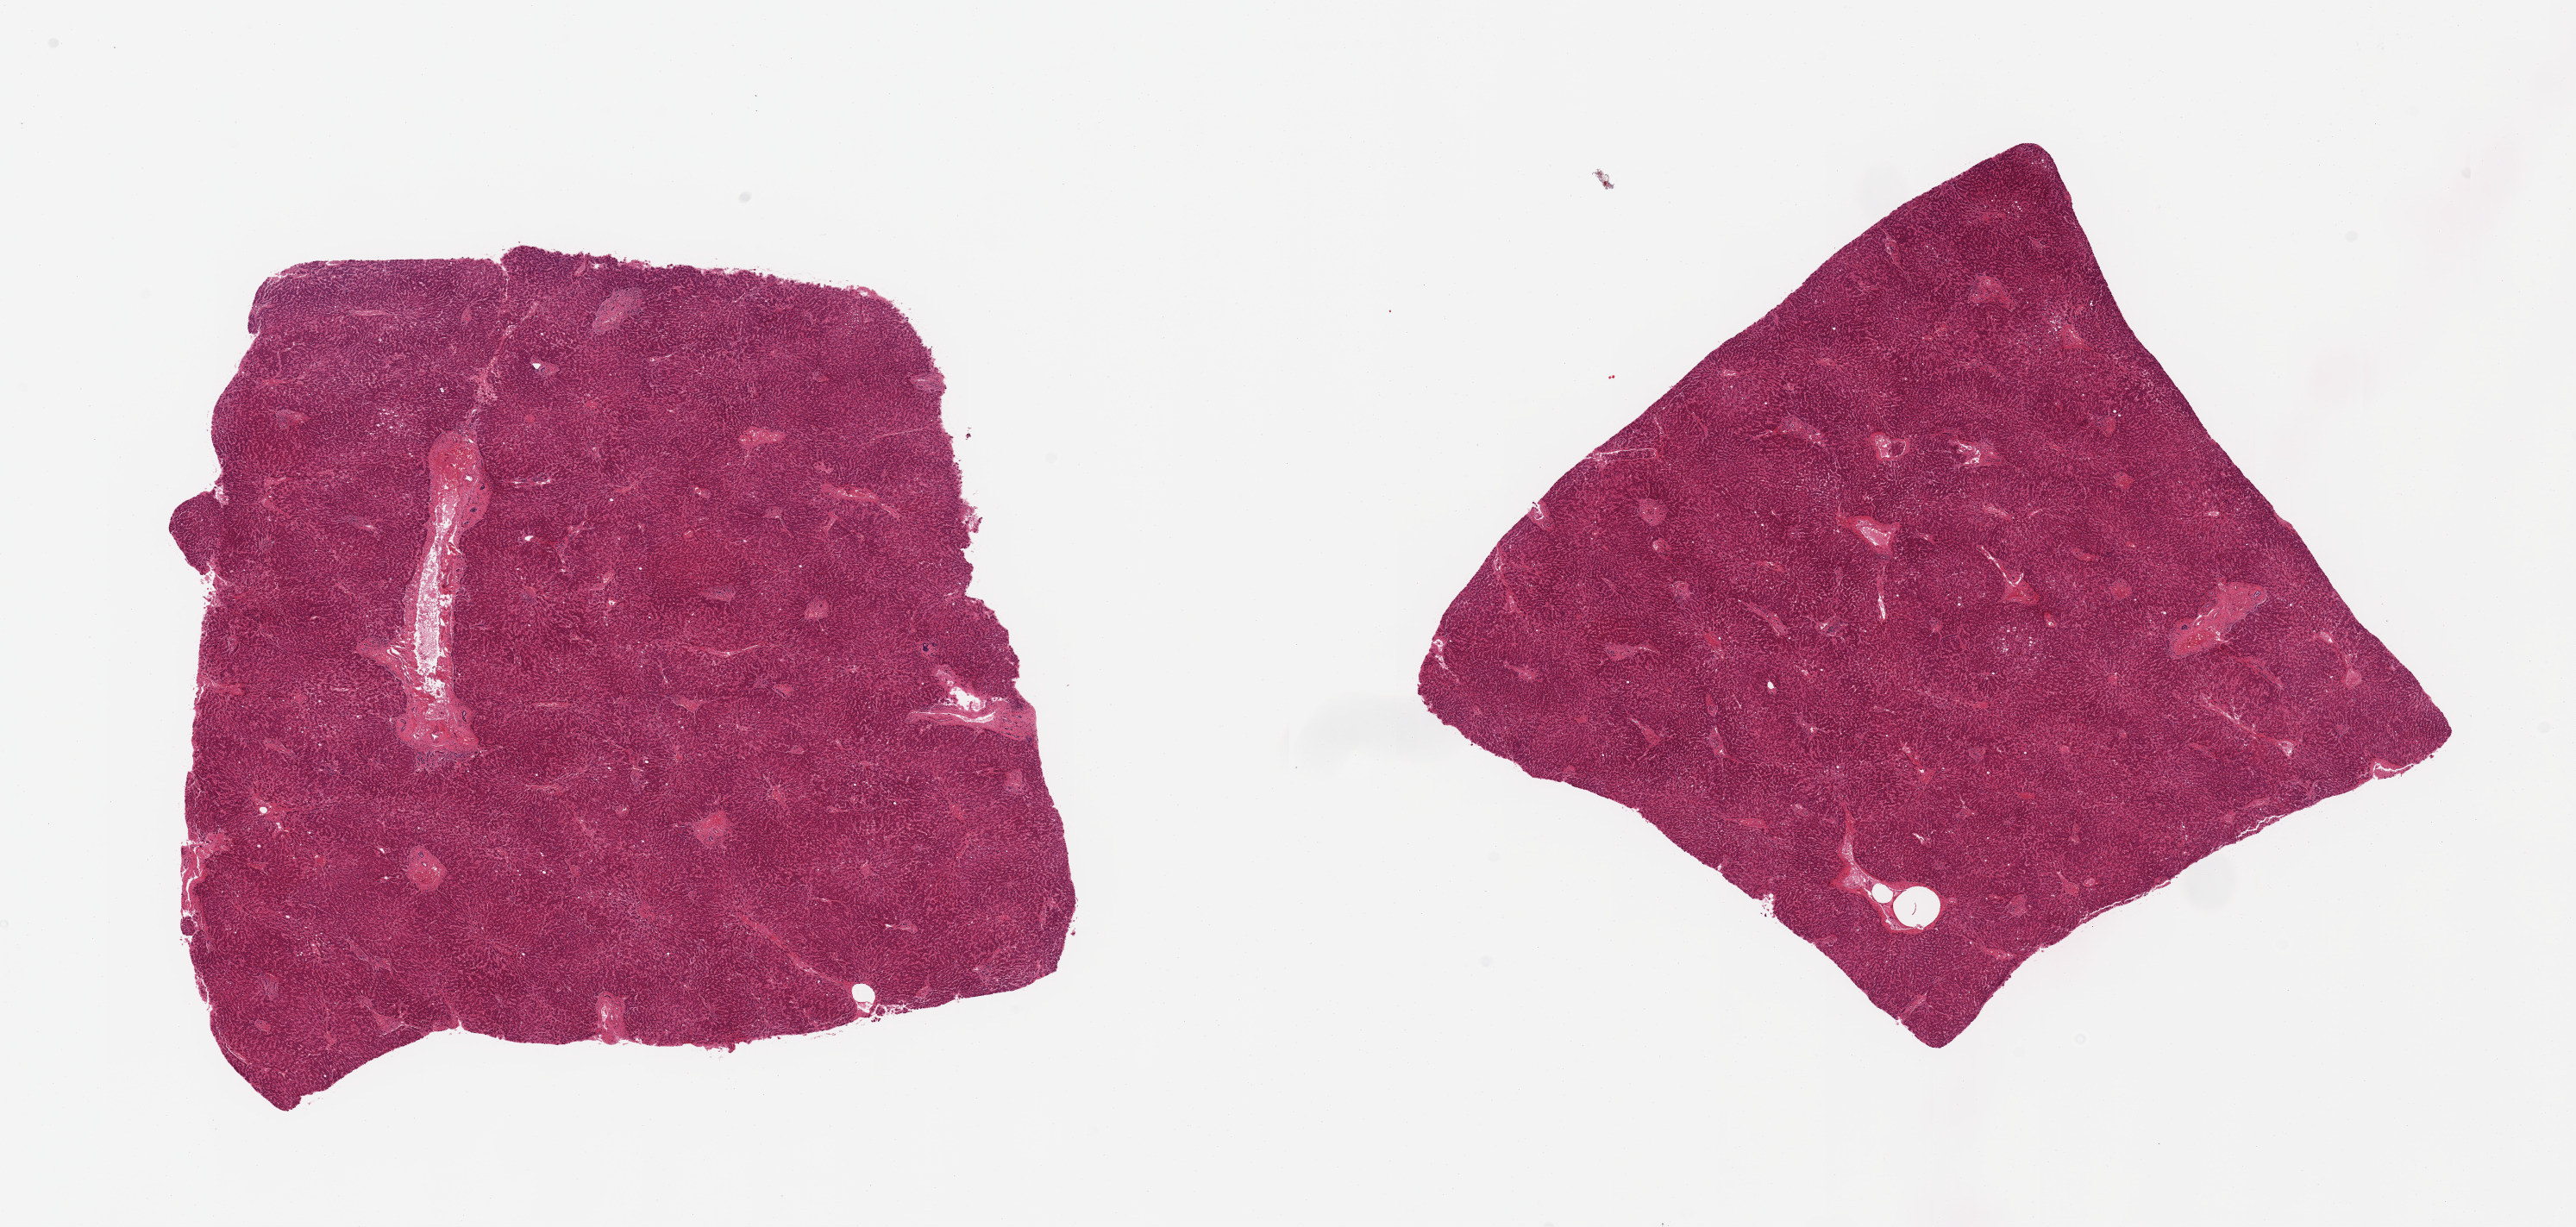
Digitized haematoxylin and eosin-stained section, brightfield — whole scanned area (about 23.6 x 11.3 mm) shown as a low-resolution overview, PAXgene-fixed paraffin-embedded (PFPE) section, sampled site (target tissue): liver, donor tissue sample. Donor sex: male.
Reviewer comment on this tissue sample: 2 pieces; mild congestion; <5% macrovesicular steatosis.